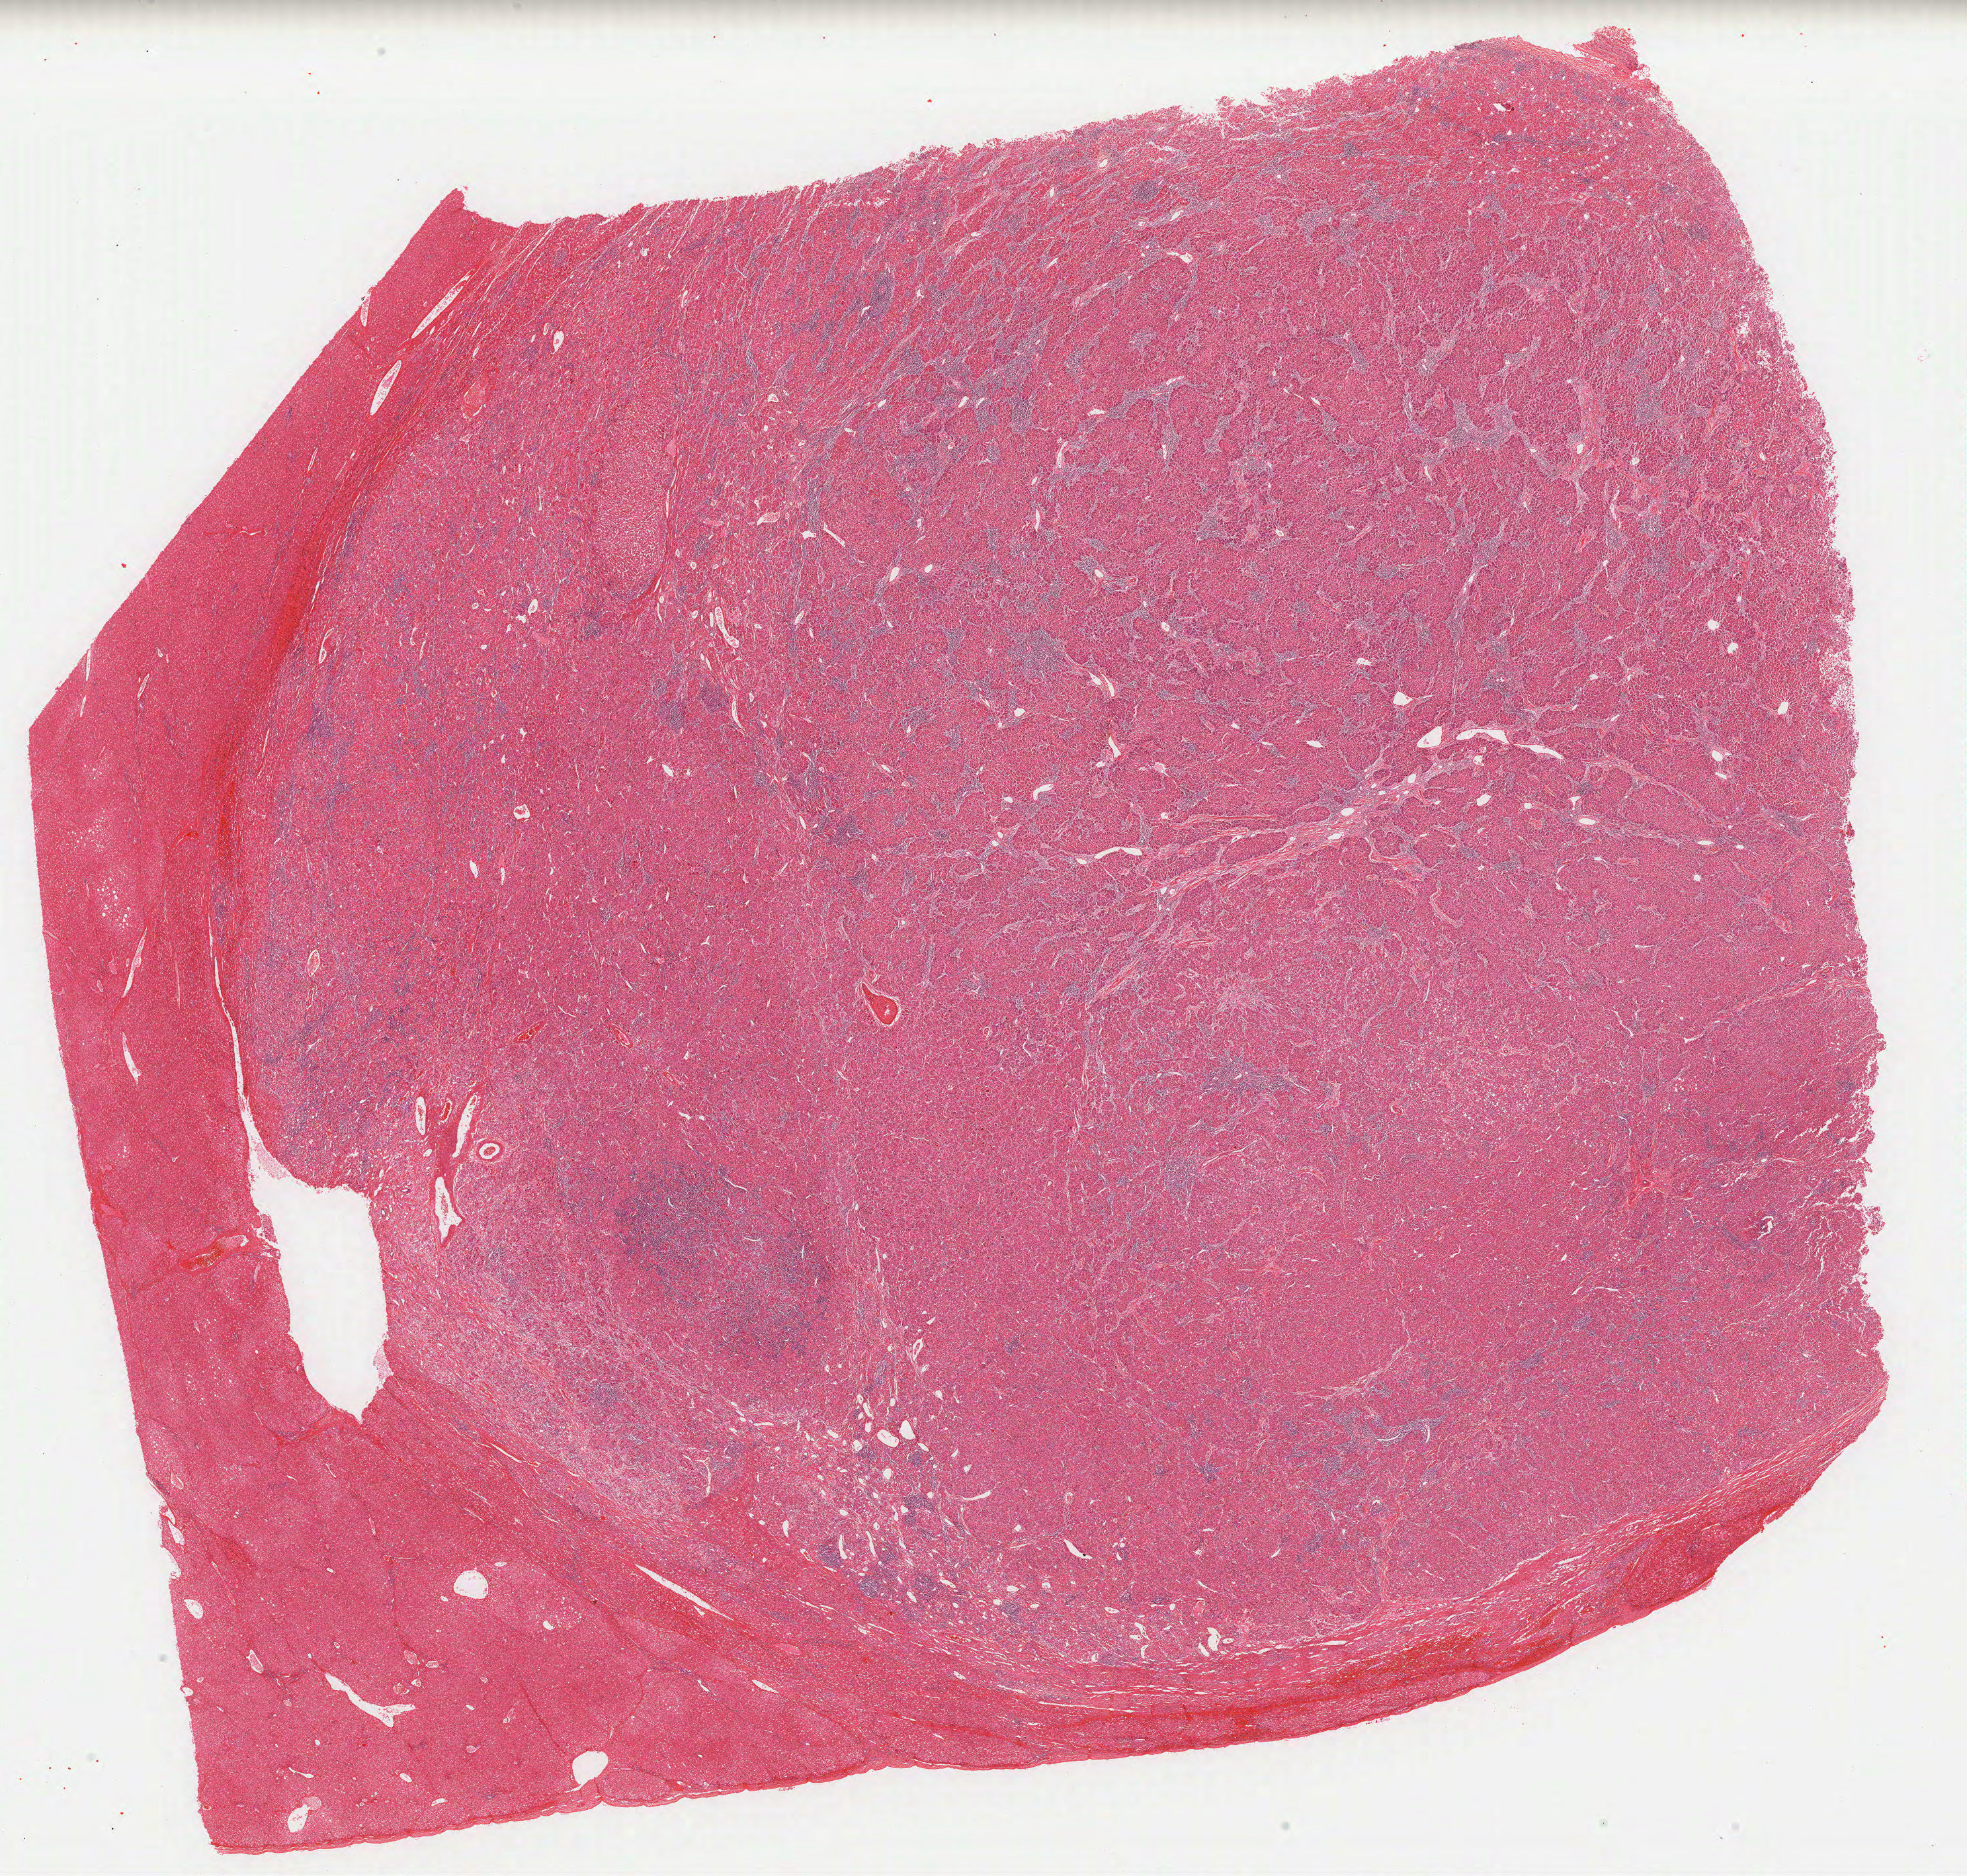
Whole-slide histology image, Hematoxylin and eosin (H&E) stained — whole scanned area (about 23.5 x 22.4 mm, slide scanned at 40x) shown as a low-resolution overview; FFPE section; sample: primary tumour, liver. Patient: male, age at initial diagnosis 44 years. Histologic grade: G2 (moderately differentiated).
• pathologic diagnosis: Hepatocellular carcinoma, NOS
• AJCC pathologic stage: I (6th edition)